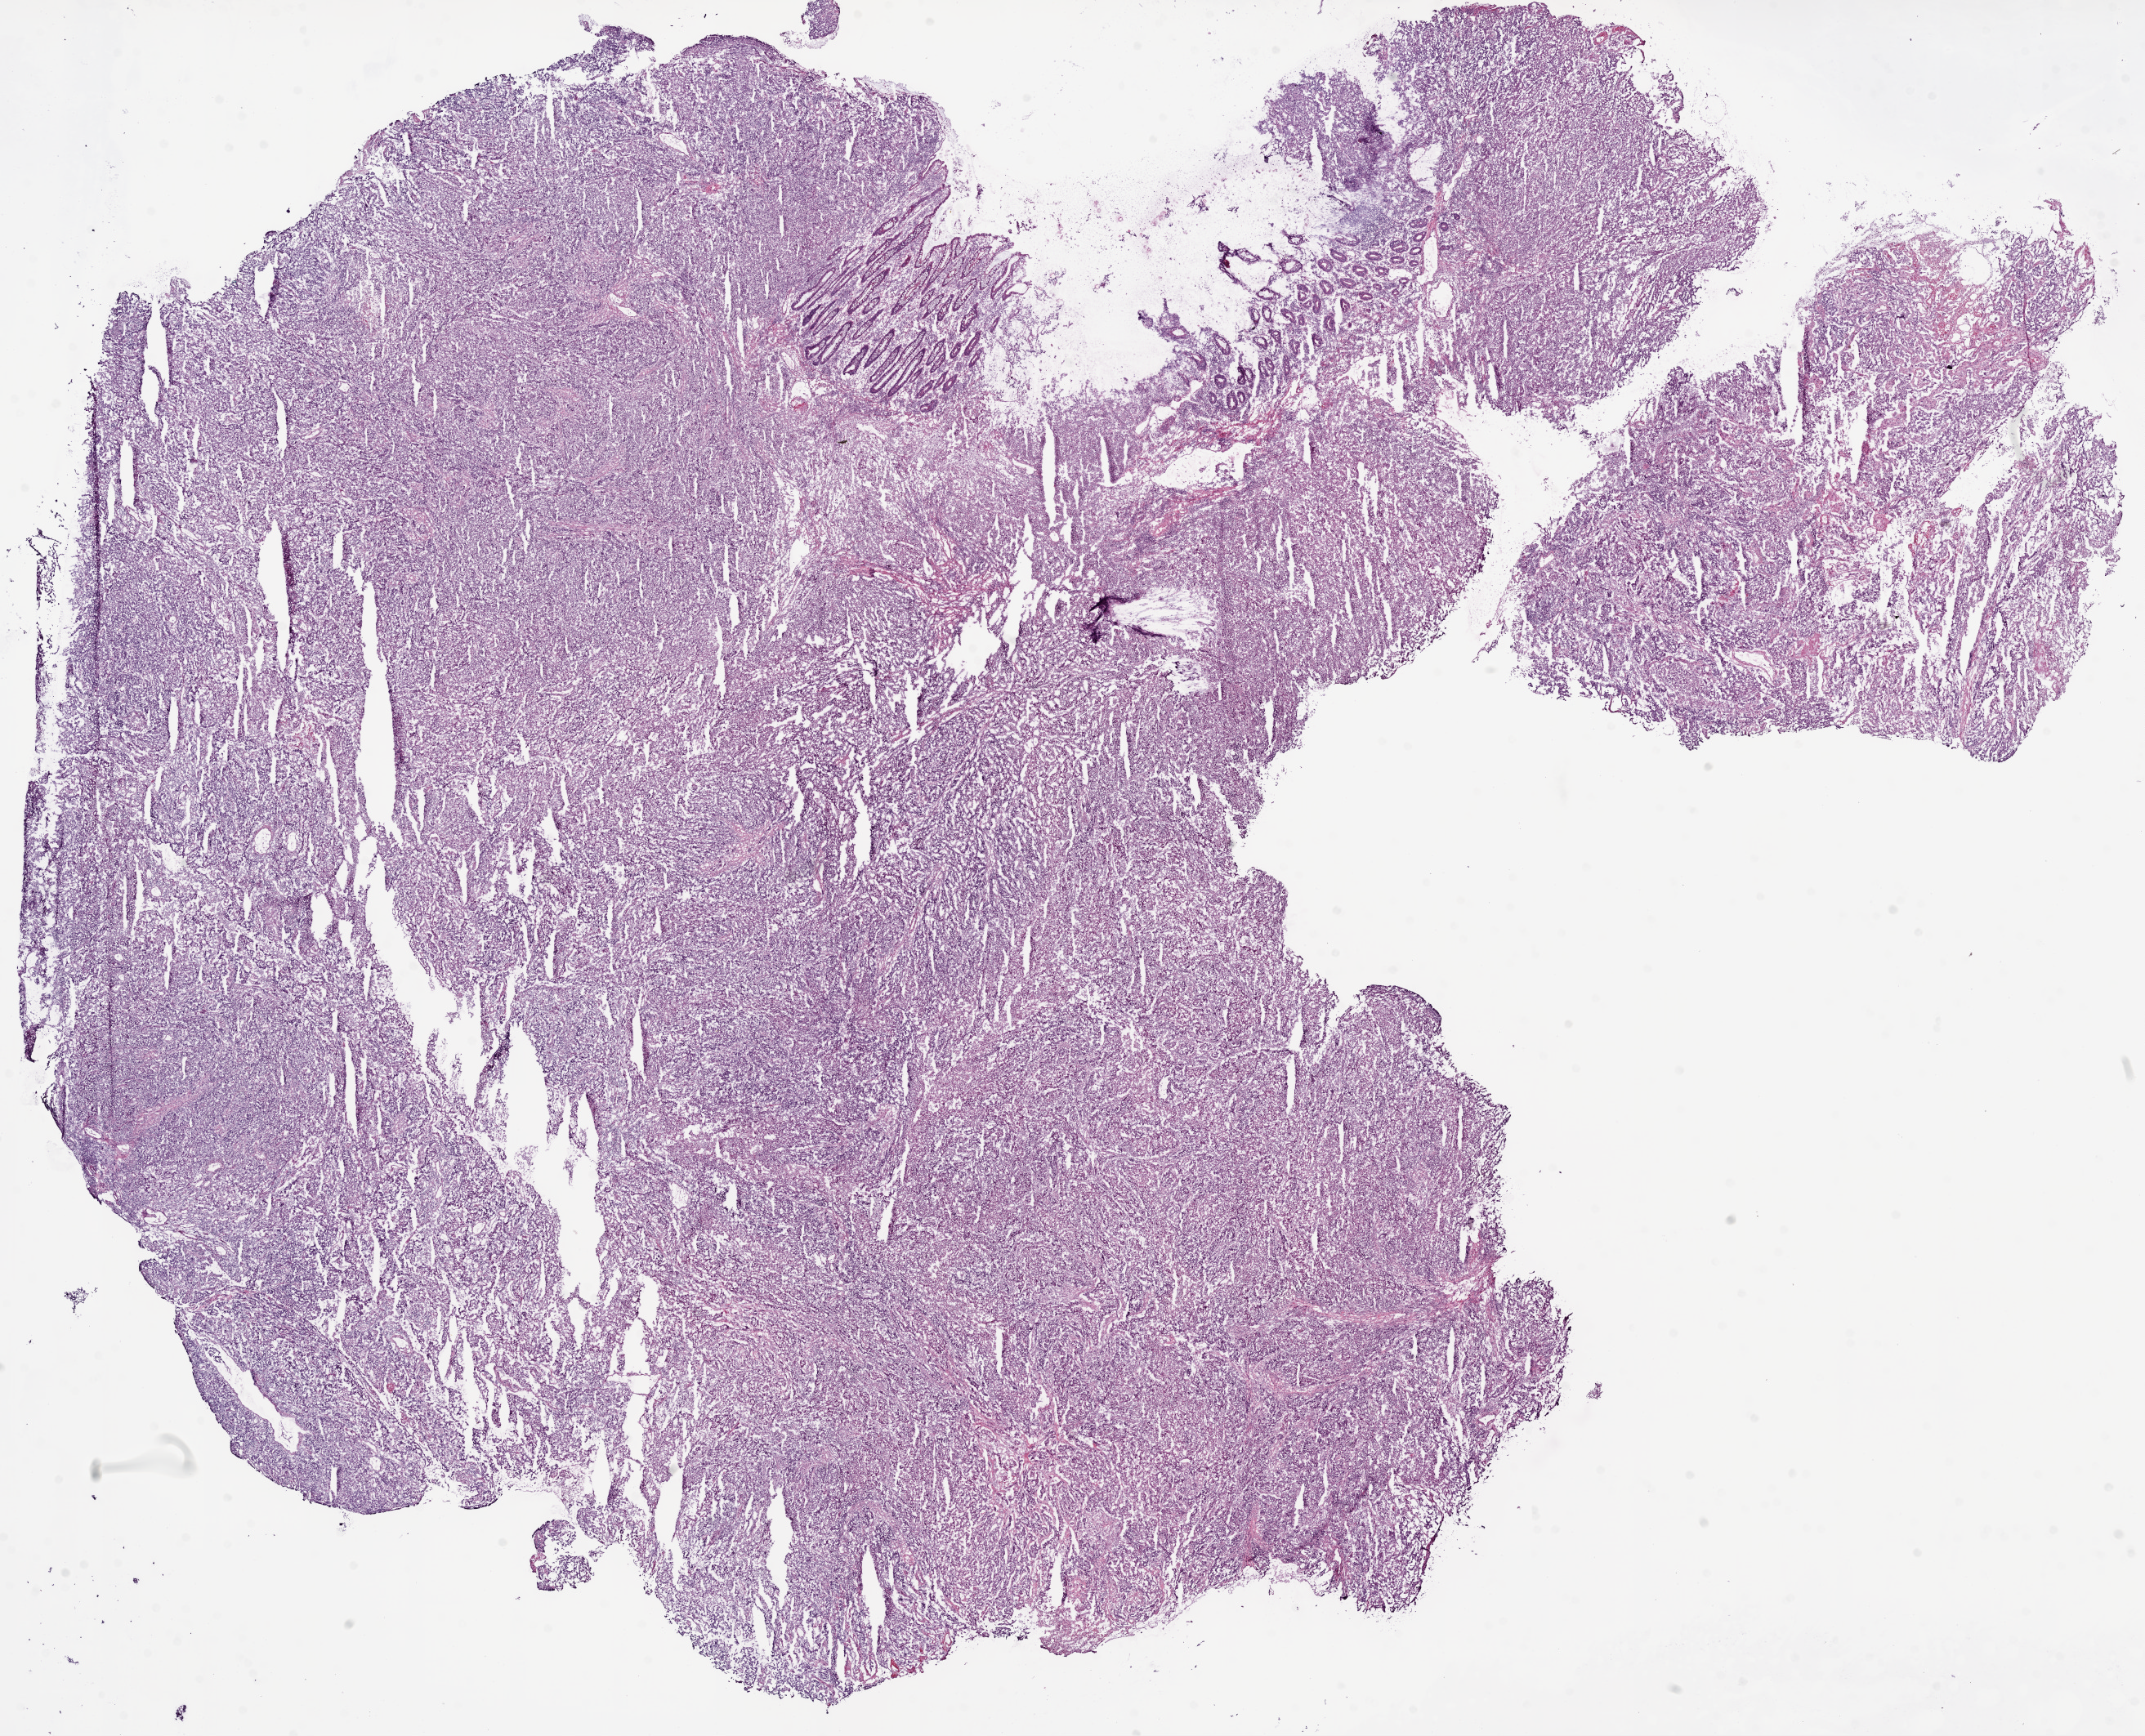
Whole-slide histology image, Hematoxylin and eosin (H&E) stained — shown as a low-resolution overview of the whole scanned area (about 21.1 x 17.1 mm); frozen section from the bottom of the tissue portion; colon, primary tumour sample. Male, age 69 years at initial diagnosis. Composition of this section per pathologist review: tumour cells 89%, tumour nuclei 65%, normal cells 3%, stromal cells 5%, necrosis 3%.
AJCC pathologic stage: IIA. Histologic diagnosis: Adenocarcinoma, NOS (ascending colon).